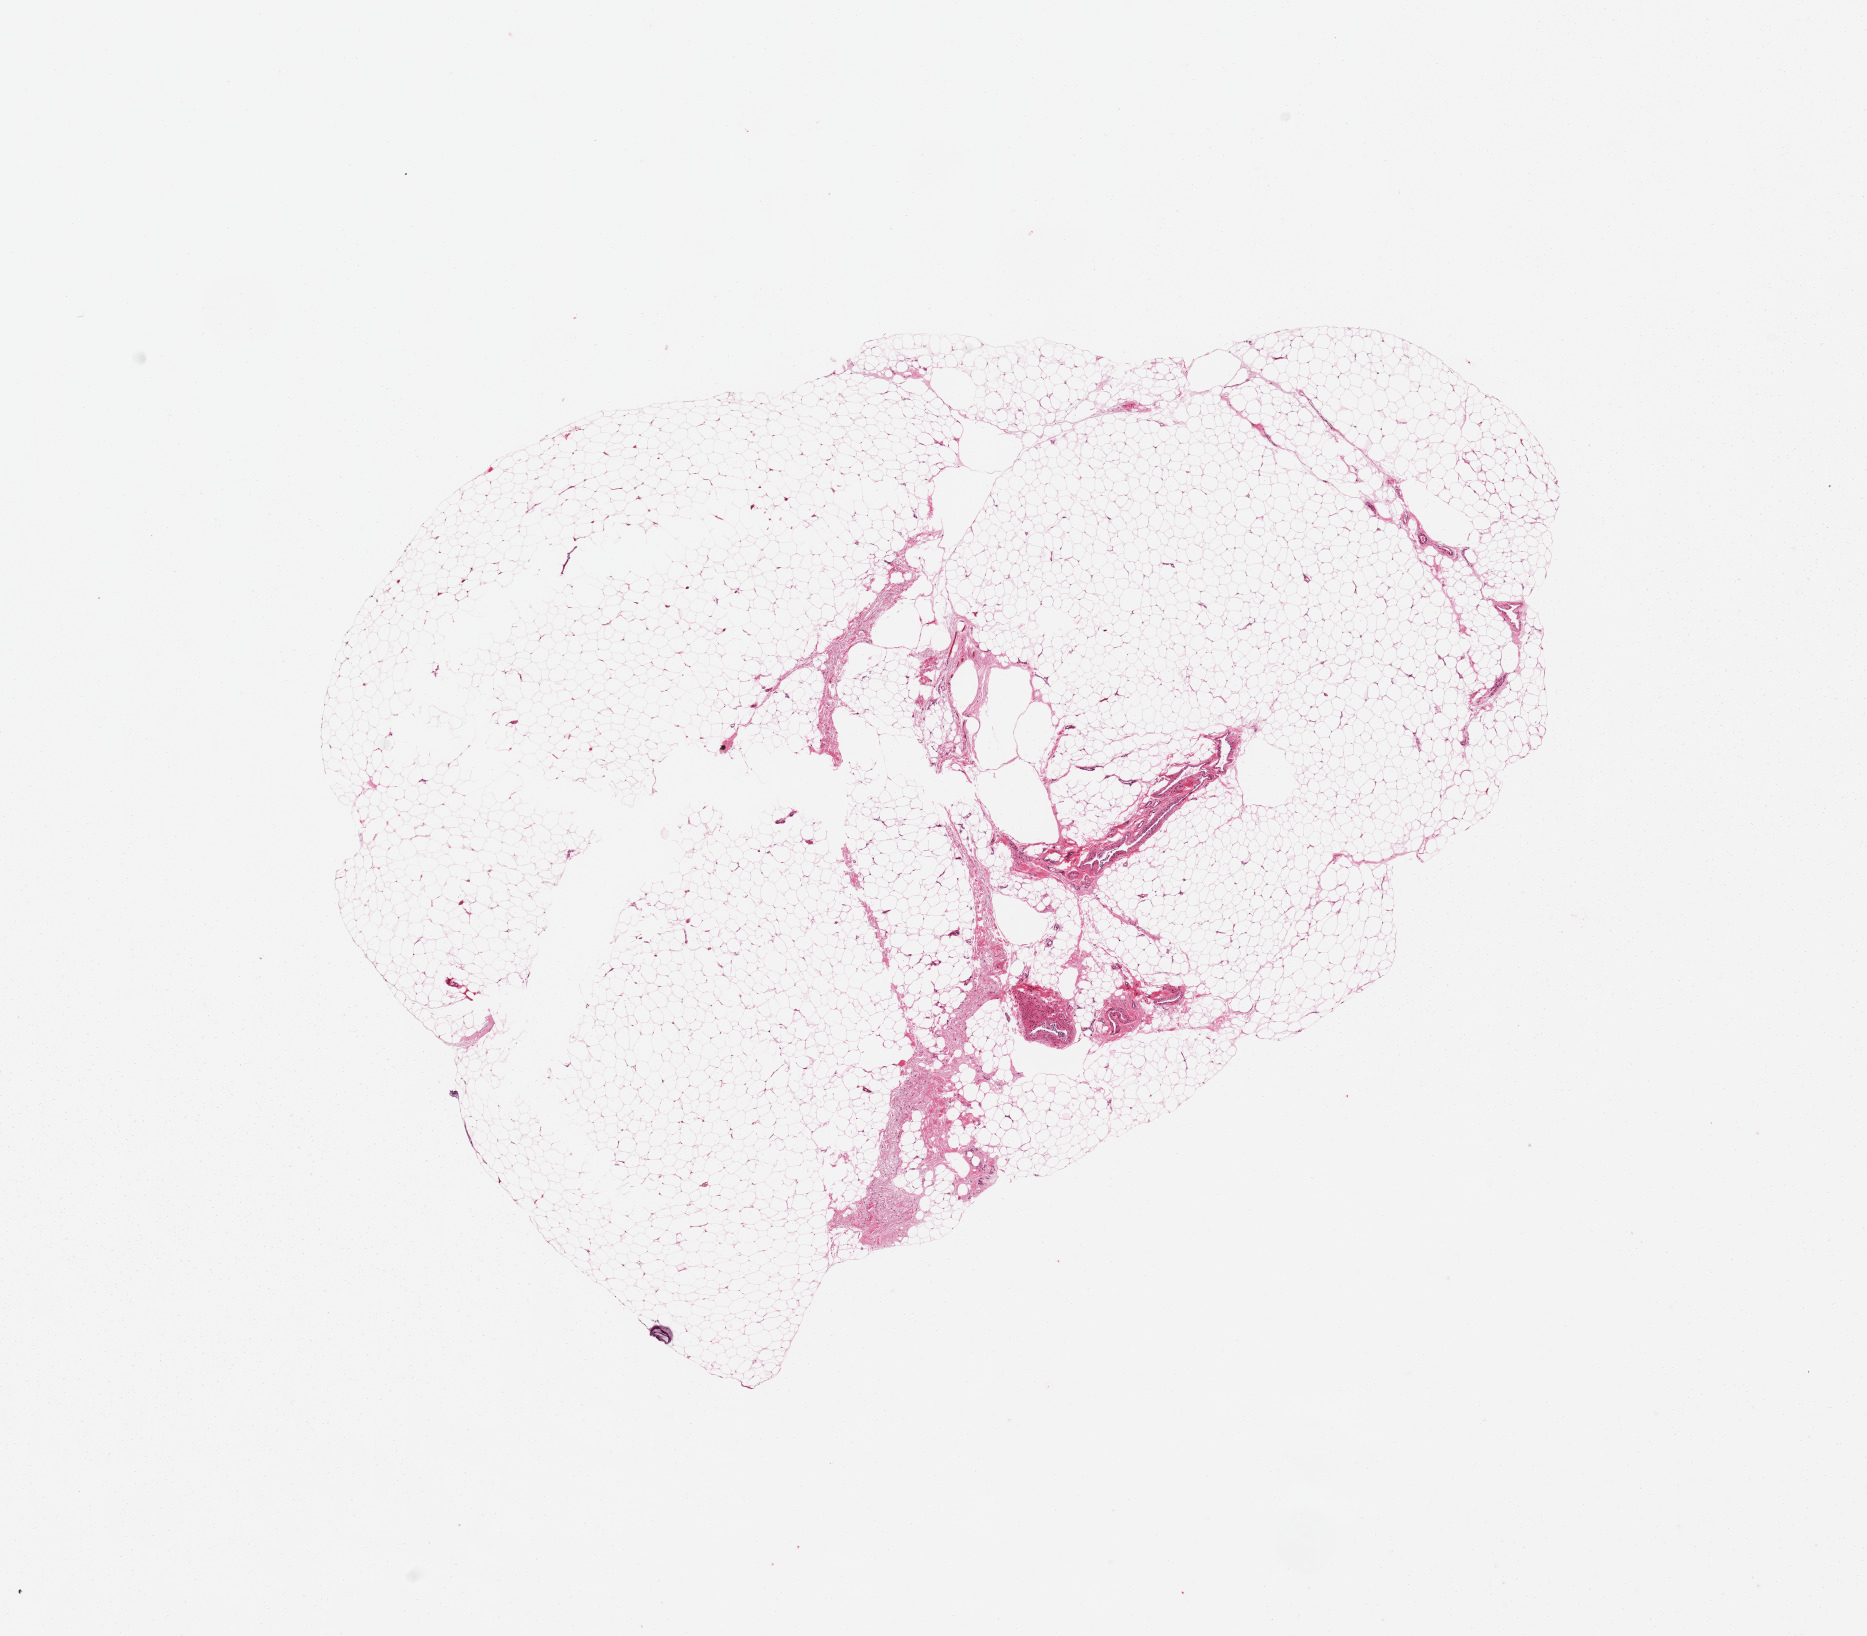
Whole-slide image, haematoxylin and eosin stain, brightfield, a low-resolution overview of the entire scanned area, about 14.8 x 12.9 mm; PAXgene-fixed, paraffin-embedded tissue; sampled site (target tissue): adipose tissue; donor tissue sample.
Reviewer comment on this tissue sample: 10x7mm aliquot. Small central area is under-fixed.